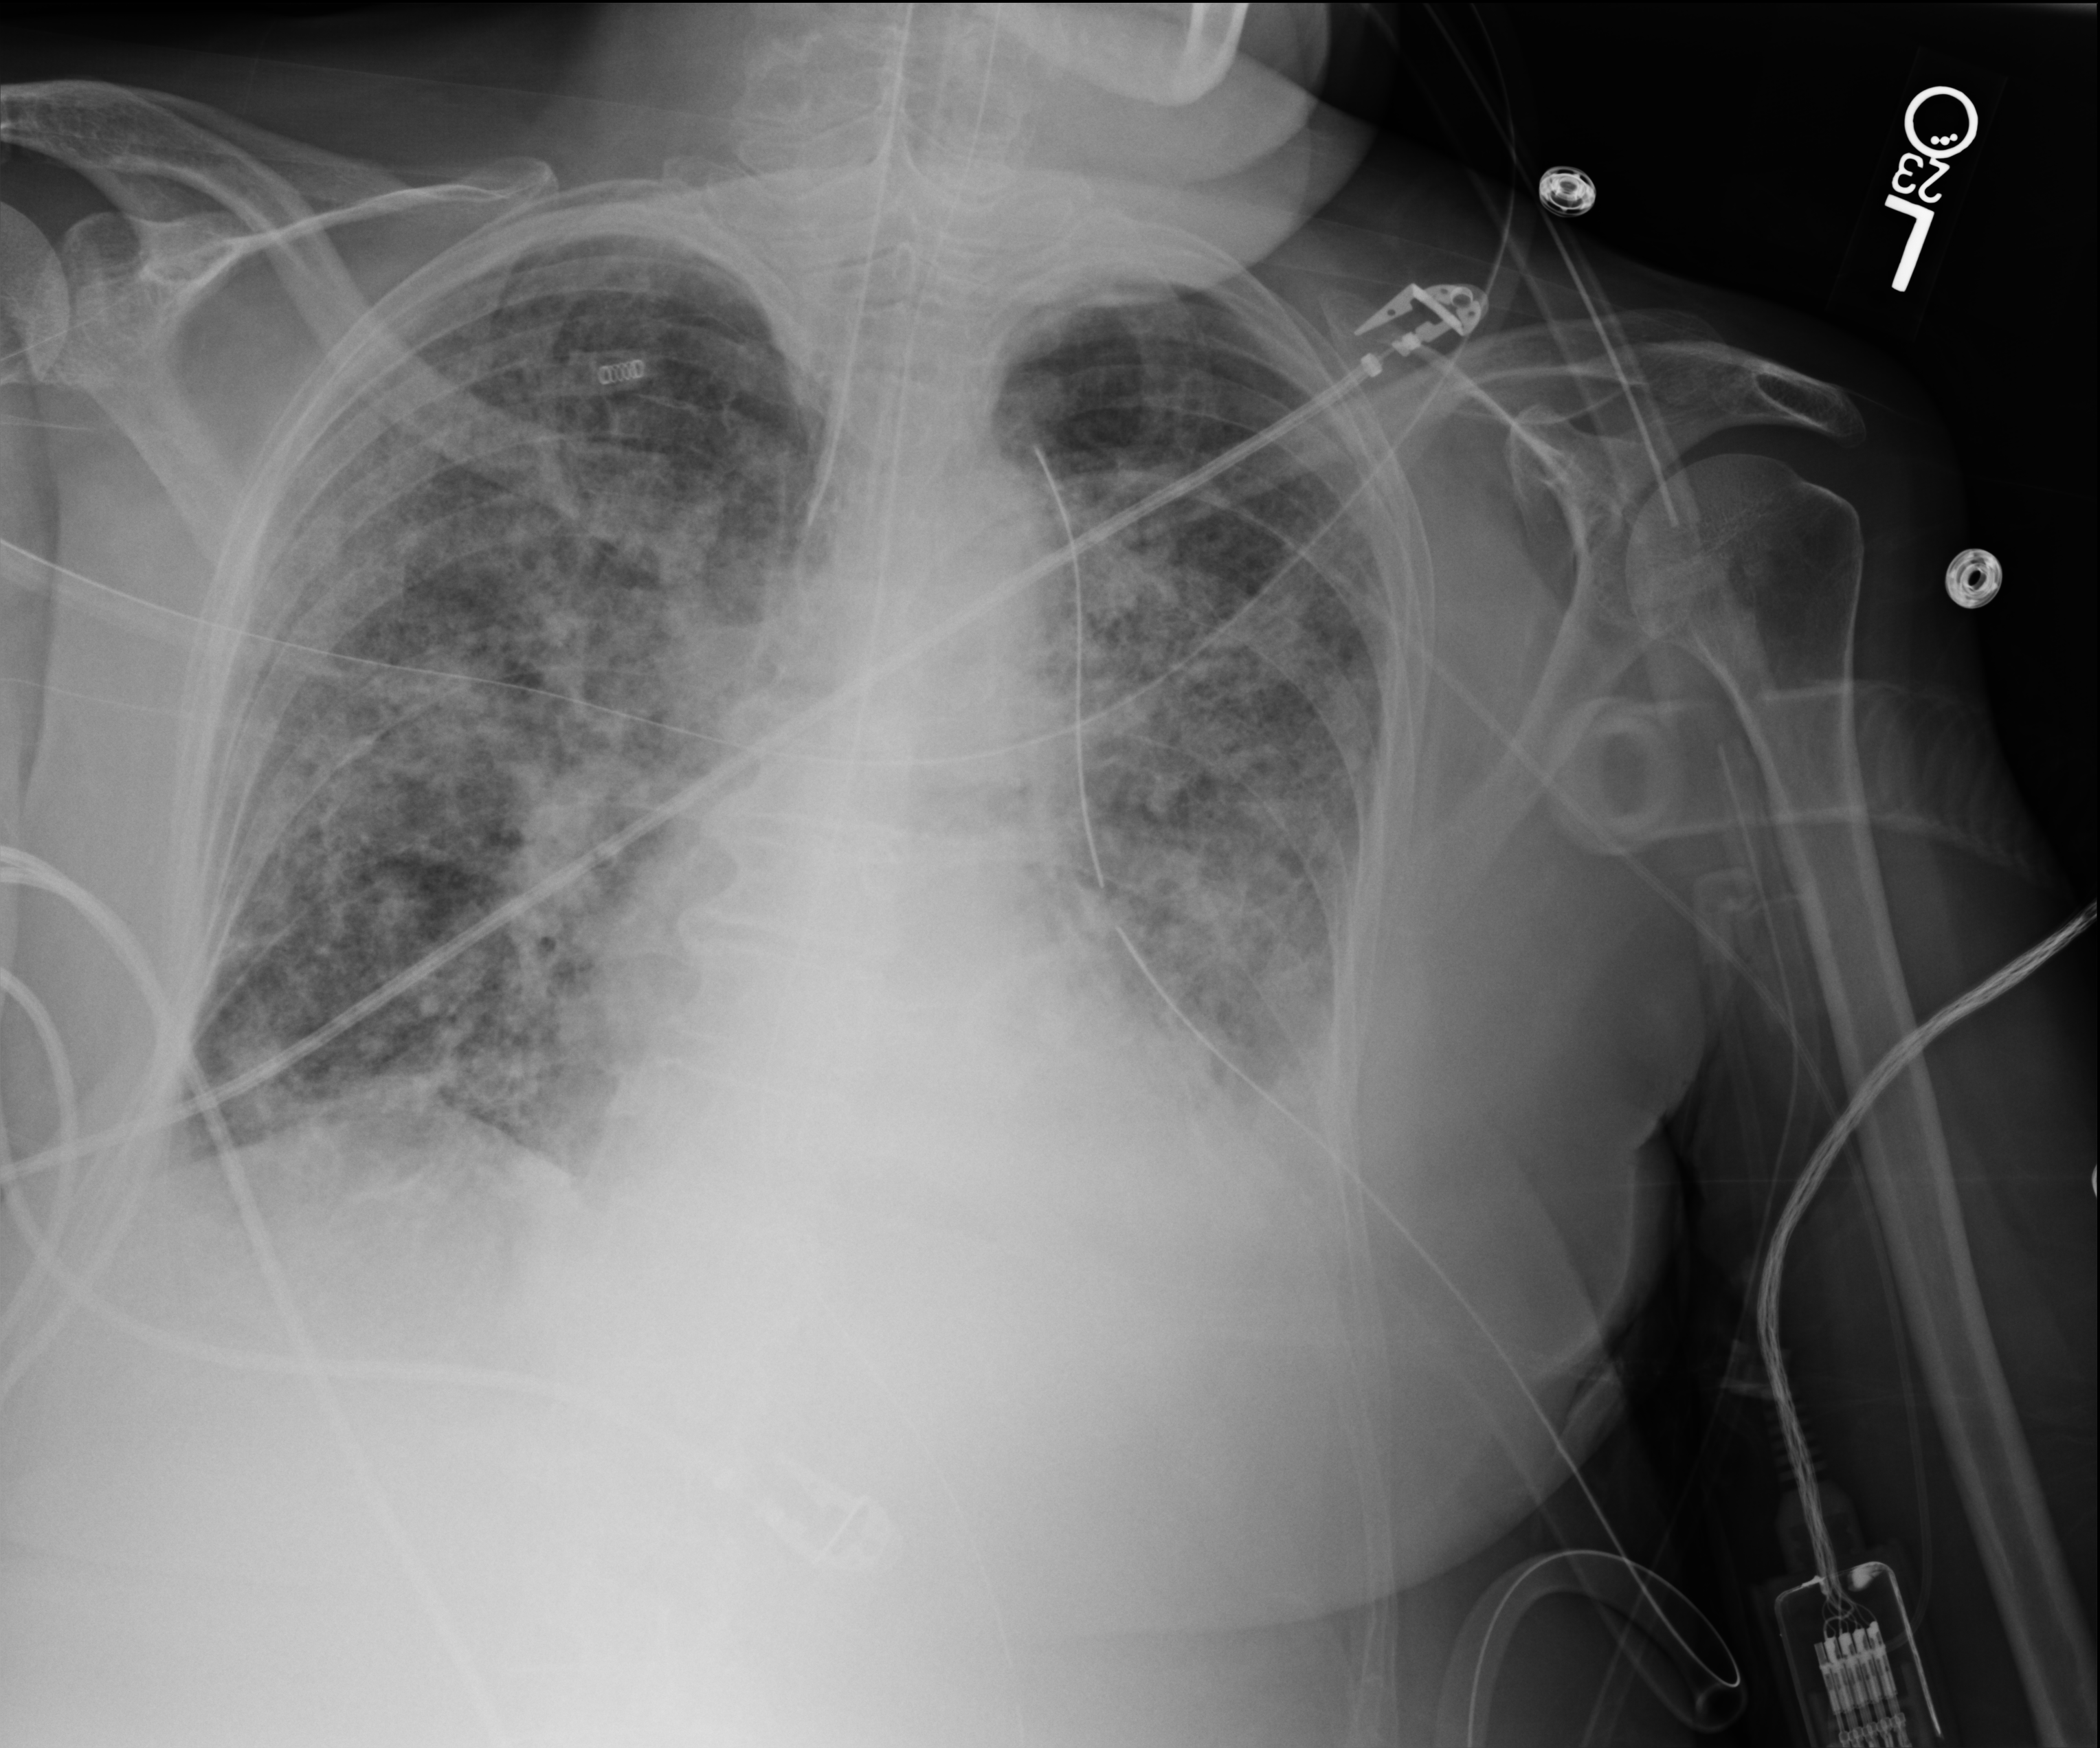
Chest X-ray (portable), anteroposterior (AP) projection. Patient hospitalised with COVID-19; female, aged 75–90 years.
Admission-level facts for this patient (not findings on this image; timing relative to this image not recorded):
- mechanically ventilated during this hospital stay: yes